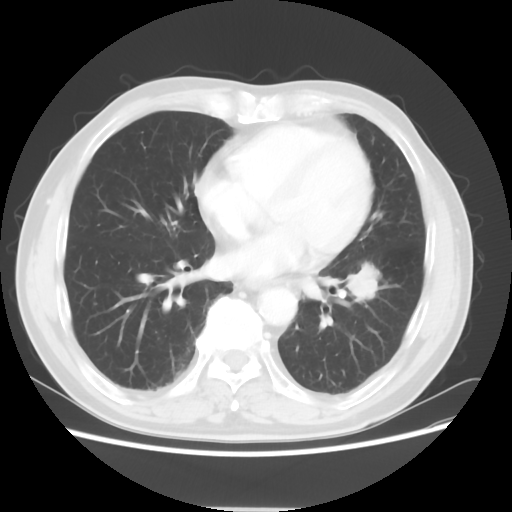
Chest CT, one axial slice. Reconstruction kernel STANDARD. 120 kVp. Lung window (W 1500 / L -600 HU). 5 mm slice thickness. 512 × 512 image matrix, field of view 366 × 366 mm. Male patient, age 71 years. Case-level facts recorded for this patient, not image findings: clinical TNM (as recorded): T1c N1 M0; histopathological grade: G2-3.
Structures marked on this image (bounding box drawn by a radiologist):
- lung tumour (recorded histology: adenocarcinoma): box from (x=342, y=254) to (x=381, y=311) px